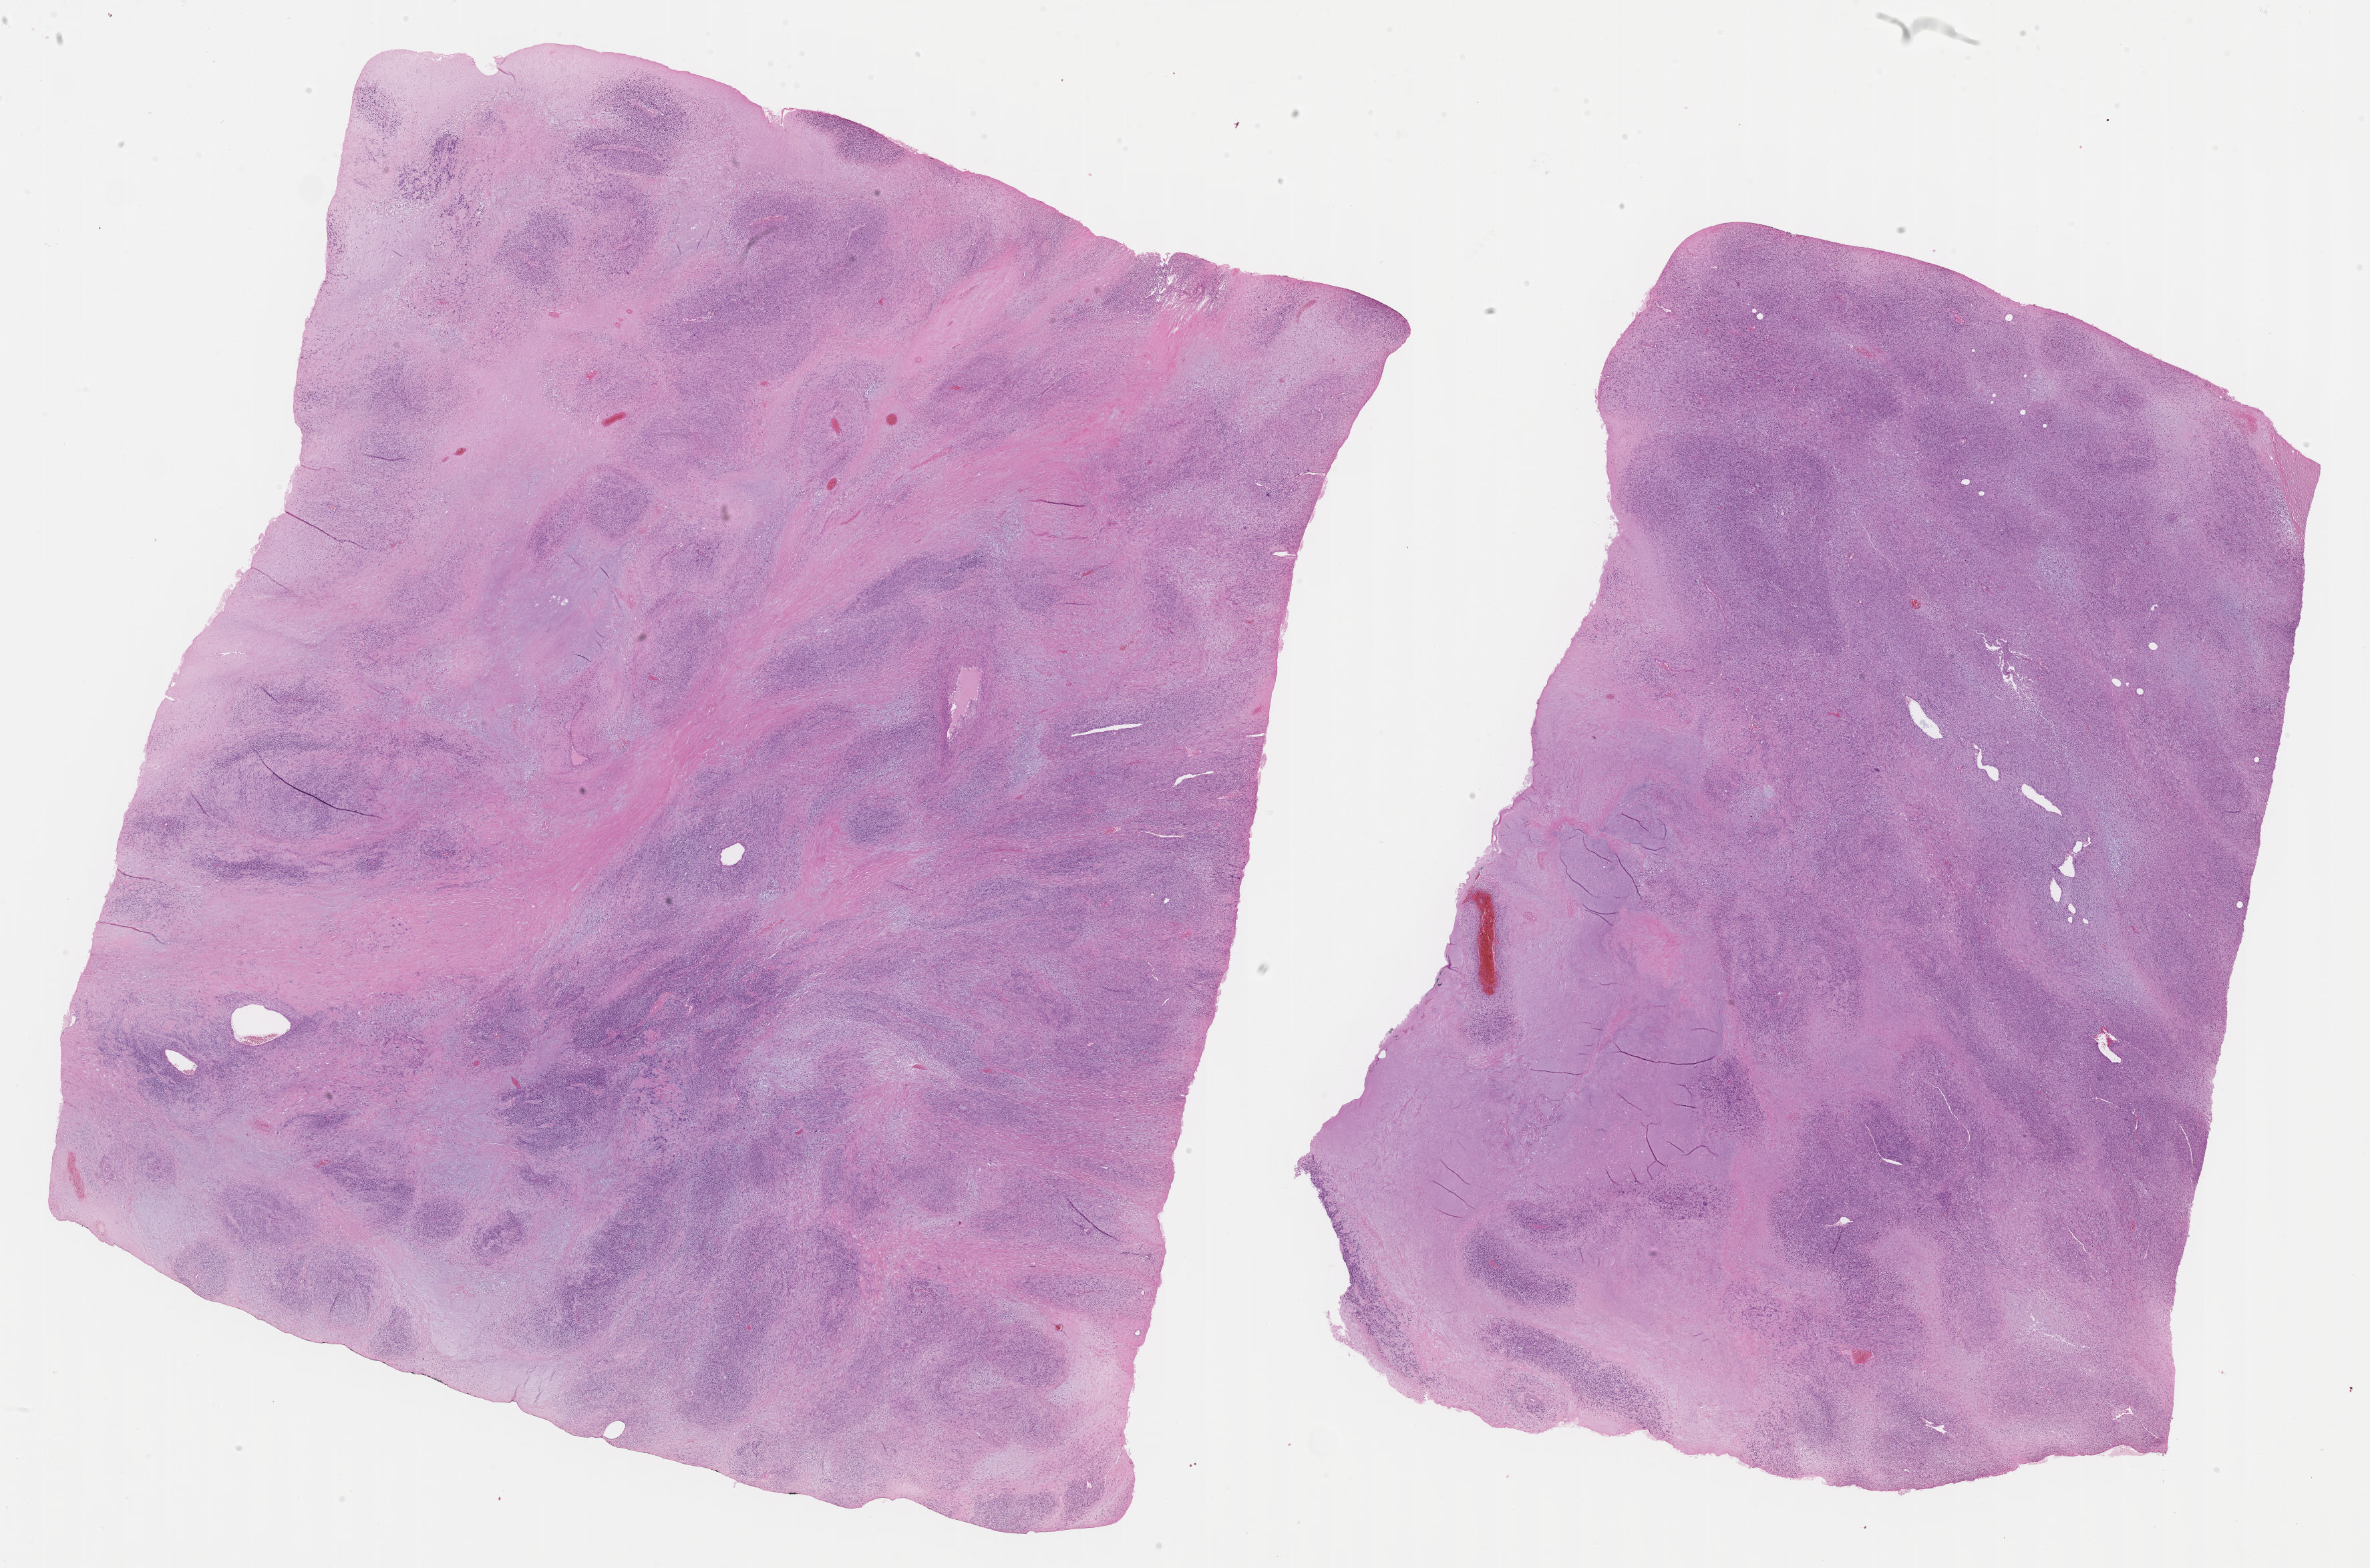
Digitized haematoxylin and eosin-stained section of tumor tissue — a low-resolution overview of the entire scanned area, about 28.7 x 19.0 mm. Formalin-fixed, paraffin-embedded (FFPE) tissue. Sample anatomic site: abdomen. Male patient, age at diagnosis 3.3 years.
Stage (as recorded): 4. Primary site (case record): pelvis, site indeterminate. Diagnosis: rhabdomyosarcoma; histological classification: spindle cell rhabdomyosarcoma. Metastatic status at presentation (as recorded): metastatic (confirmed).